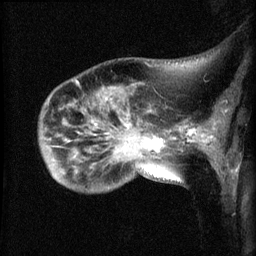
Breast MRI (dynamic contrast-enhanced), one sagittal slice. Slice 15 of 60 in the series (ordered by position). Dynamic contrast-enhanced series, image 2 of 3 at this slice position (ordered by acquisition). 1.5 T. TE 4.2 ms, TR 8.2 ms. 2.1 mm slice thickness. 256 × 256 image matrix, field of view 180 × 180 mm. Female patient, age 50 years.
Annotated regions visible in this slice (semi-automatically segmented with operator editing):
- analysis volume of interest (the breast-tissue region the enhancement analysis was run in; not a lesion): box from (x=39, y=84) to (x=169, y=192) px
- tumour enhancement mask (voxels above the 70 % enhancement threshold inside the analysis volume of interest): (x=146, y=136)–(x=164, y=153)